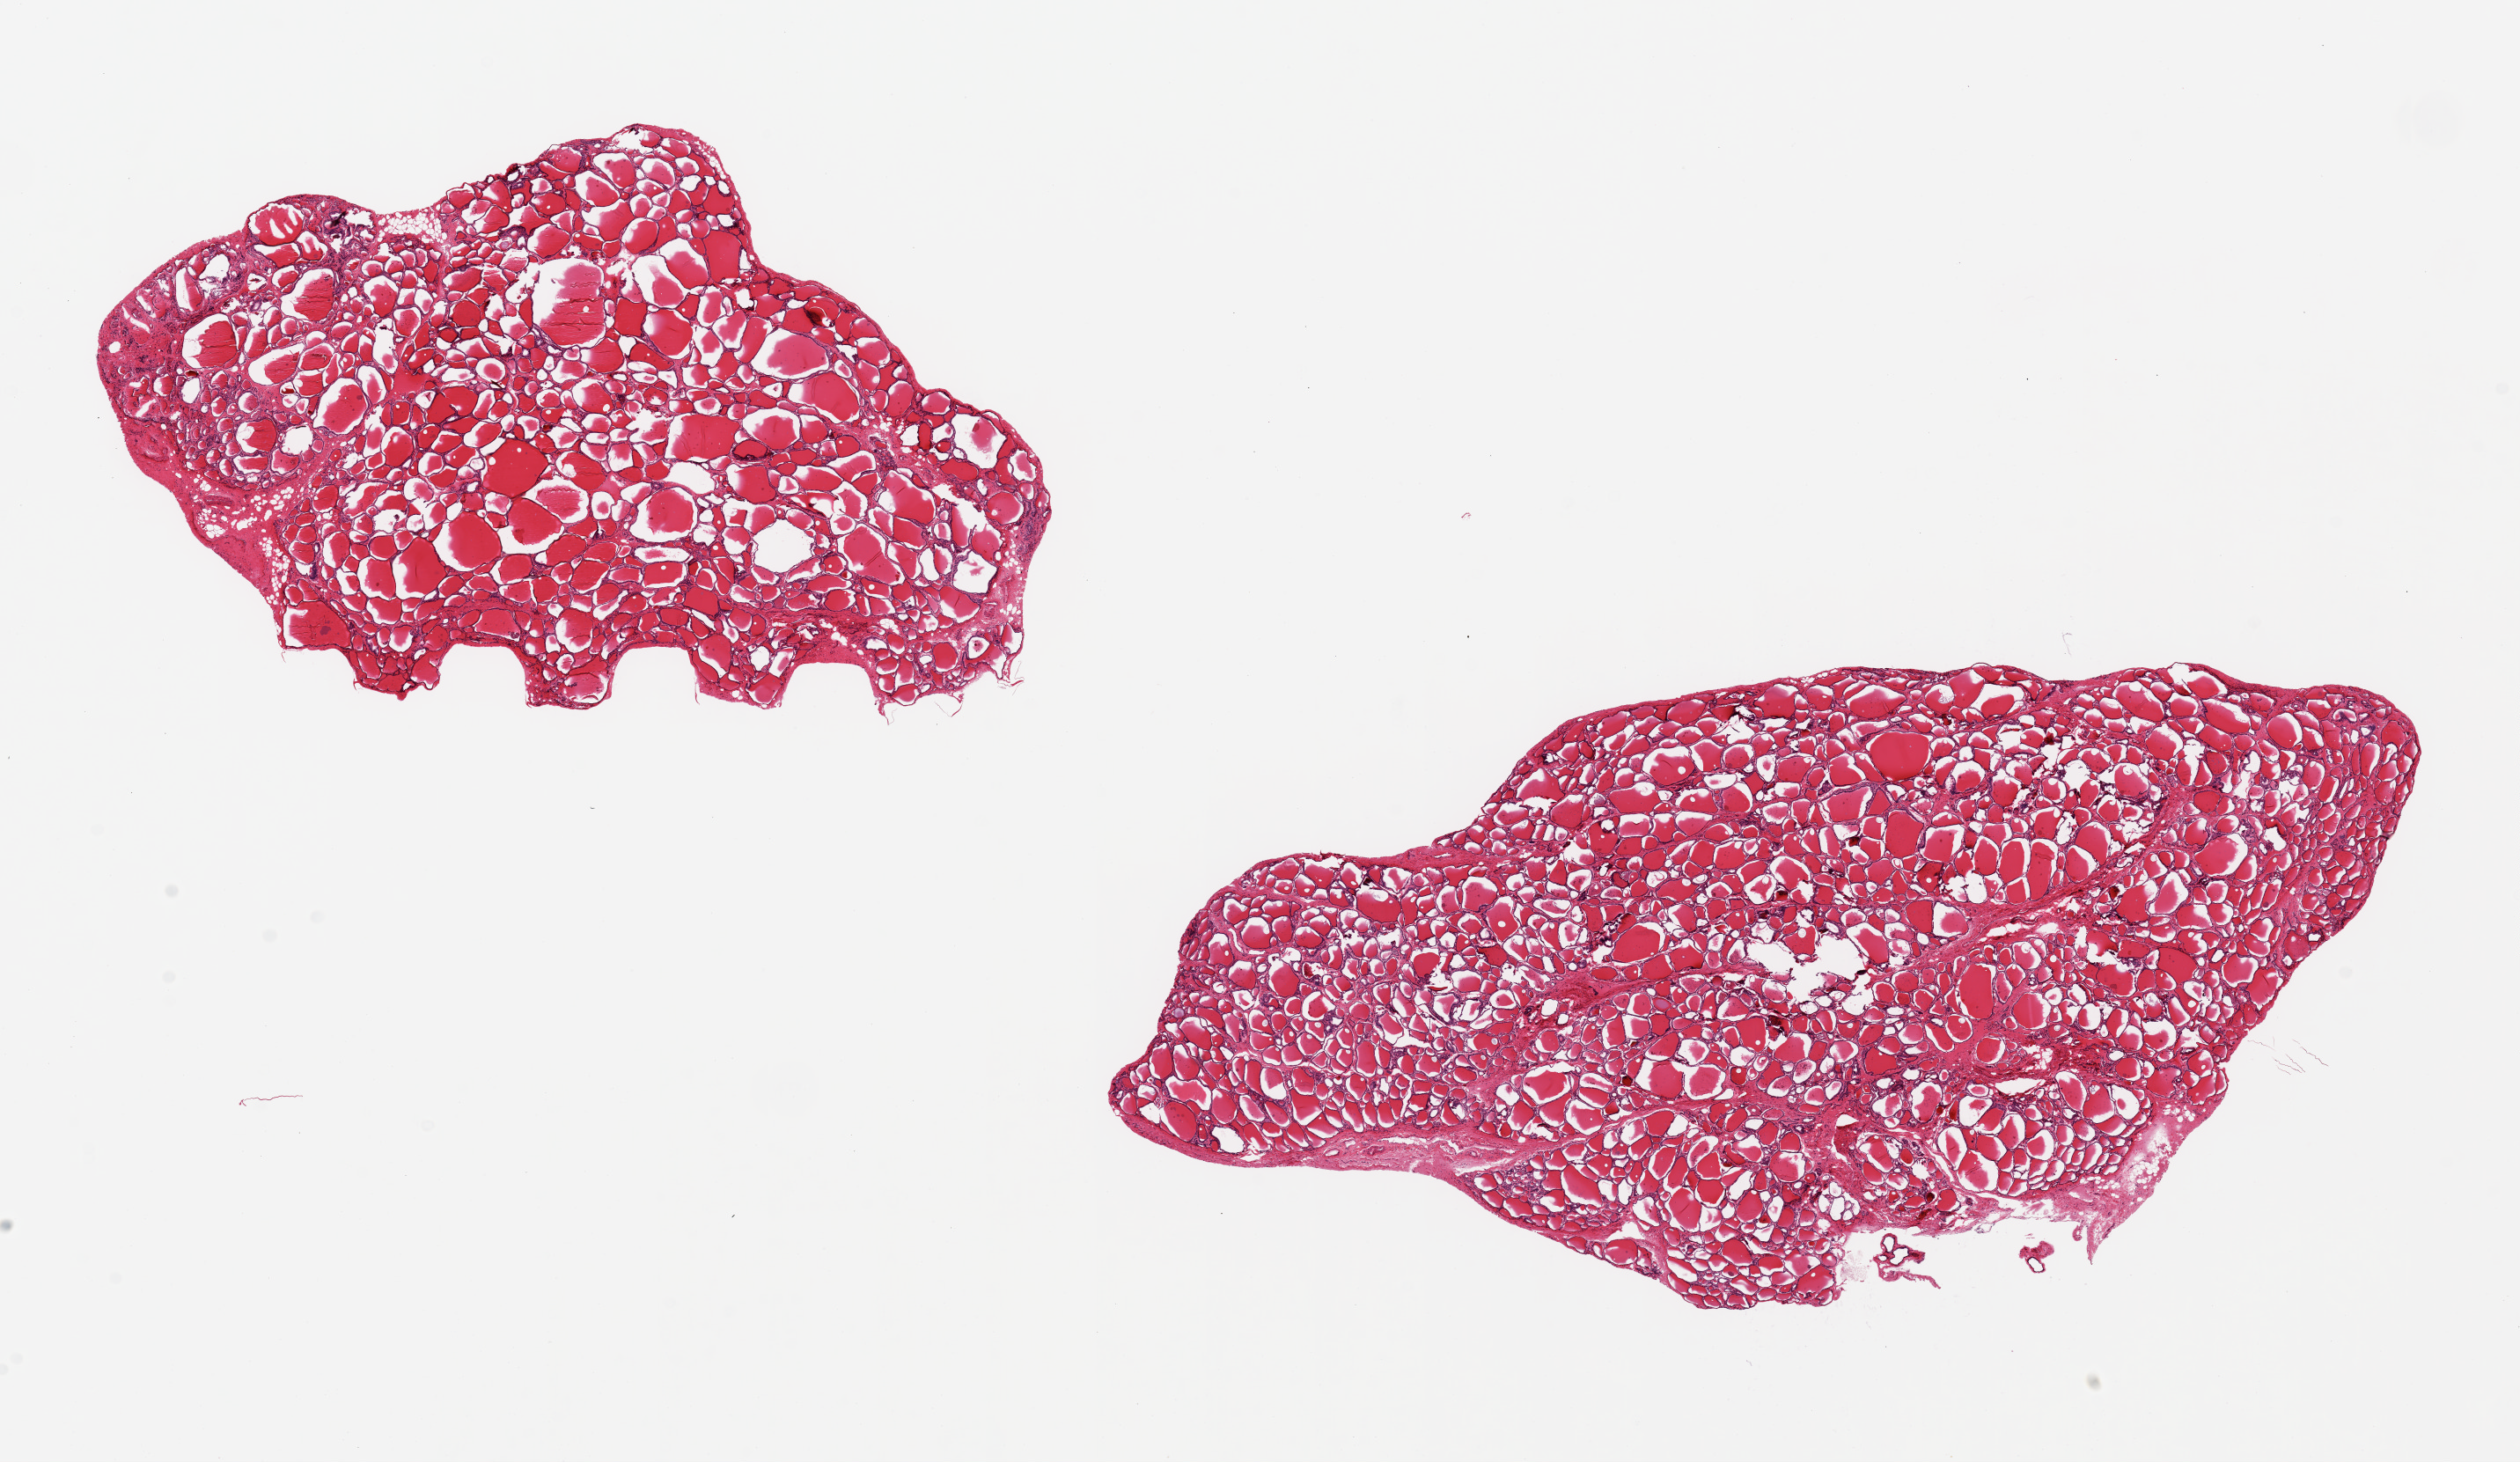
Digitized haematoxylin and eosin-stained section — shown as a low-resolution overview of the whole scanned area (about 22.6 x 13.1 mm, slide scanned at 20x), PAXgene-fixed, paraffin-embedded tissue, section of thyroid (target tissue), donor tissue sample. Donor: male.
Pathologist's review note for this sample: 2 pieces, 7x5.5 & 12X6mm;well sampled.